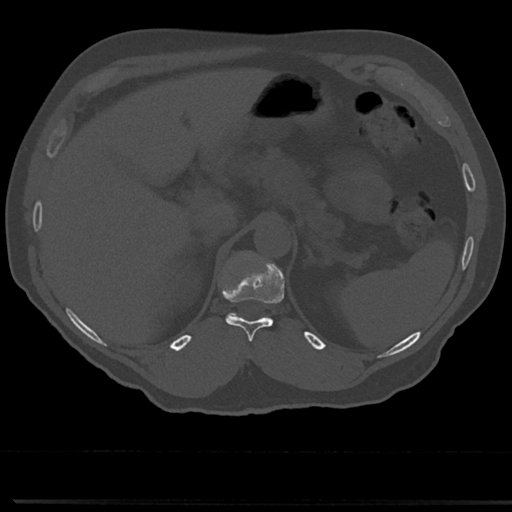
CT including the spine, one axial slice; position 189 of 817 along the scan axis; reconstruction kernel Br40s/3; bone window (W 1800 / L 400 HU); 0.5 mm slice thickness; 512 × 512 image matrix, field of view 355 × 355 mm. Male patient, age 61 years. From the clinical record (not read from this slice): primary cancer: prostate.
Outlined on this slice (semi-automatically segmented with operator editing):
- T11 vertebra: bounding box <225,269,283,343> (left, top, right, bottom; pixels)
- T12 vertebra: <228,256,255,315>